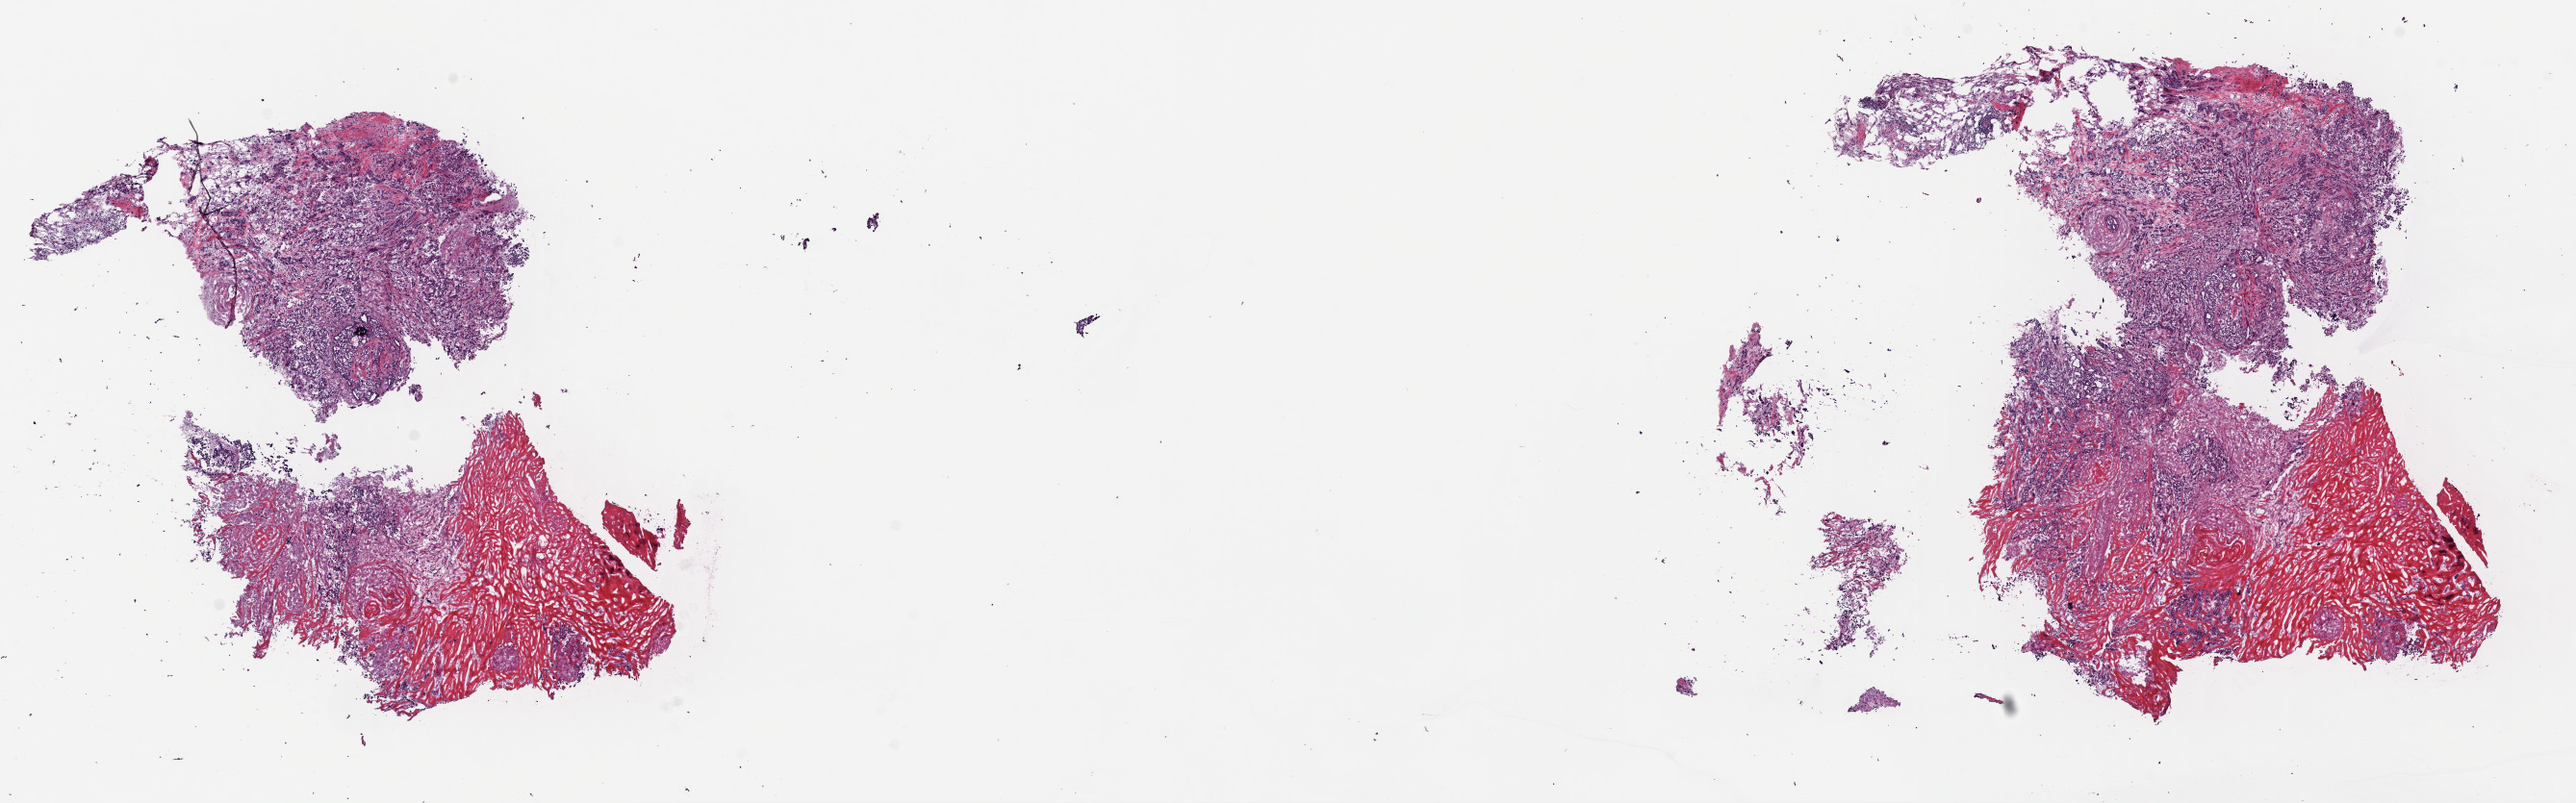
Digitized H&E tissue section (whole slide), low-resolution overview of the scanned area, about 21.1 x 6.6 mm. Frozen section from the top of the tissue portion. Sample: primary tumour, breast. Patient: female, age at initial diagnosis 72 years.
Histologic diagnosis: Infiltrating duct carcinoma, NOS.